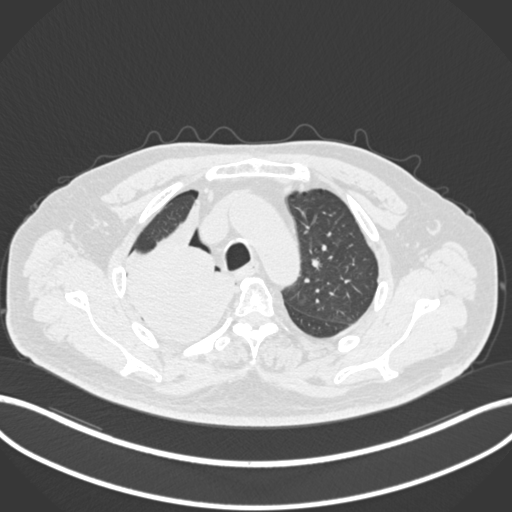
Chest CT, one axial slice; position 162 of 218 along the scan axis; reconstruction kernel B30f; 120 kVp; lung window (W 1500 / L -600 HU); 1 mm slice thickness; 512 × 512 image matrix, field of view 400 × 400 mm. Male patient, age 68 years. From the clinical record (not read from this slice): clinical TNM (as recorded): T2a N0 M0.
Structures marked on this image (rectangle marked by the reading radiologist):
- lung tumour (recorded histology: adenocarcinoma): box from (x=119, y=207) to (x=234, y=337) px